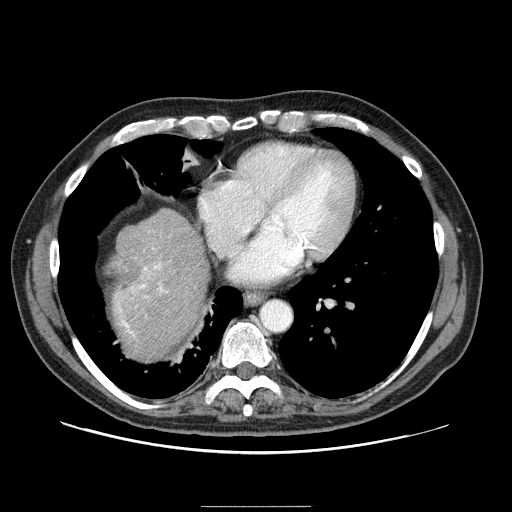
Contrast-enhanced abdominal CT (liver protocol), one axial slice; position 84 of 99 along the scan axis; reconstruction kernel STANDARD; one of 2 acquisitions stored at this slice position; soft-tissue window (W 400 / L 40 HU); 2.5 mm slice thickness; 512 × 512 image matrix, field of view 400 × 400 mm. From the clinical record (not read from this slice): diagnosis: hepatocellular carcinoma (patient treated with transarterial chemoembolisation; whether this scan precedes or follows treatment is not stated here); TNM stage (as recorded): Stage-II; Child-Pugh class: A; tumour nodularity: multinodular; tumour size: 3.2 cm.
Annotated regions visible in this slice (semi-automatically segmented with operator editing):
- liver parenchyma outside the tumour (the mass and vessels are separate outlines, so this box may not span the whole liver): bounding box [x1, y1, x2, y2] px = [112, 208, 208, 358]
- liver vessels: [118, 262, 164, 336]